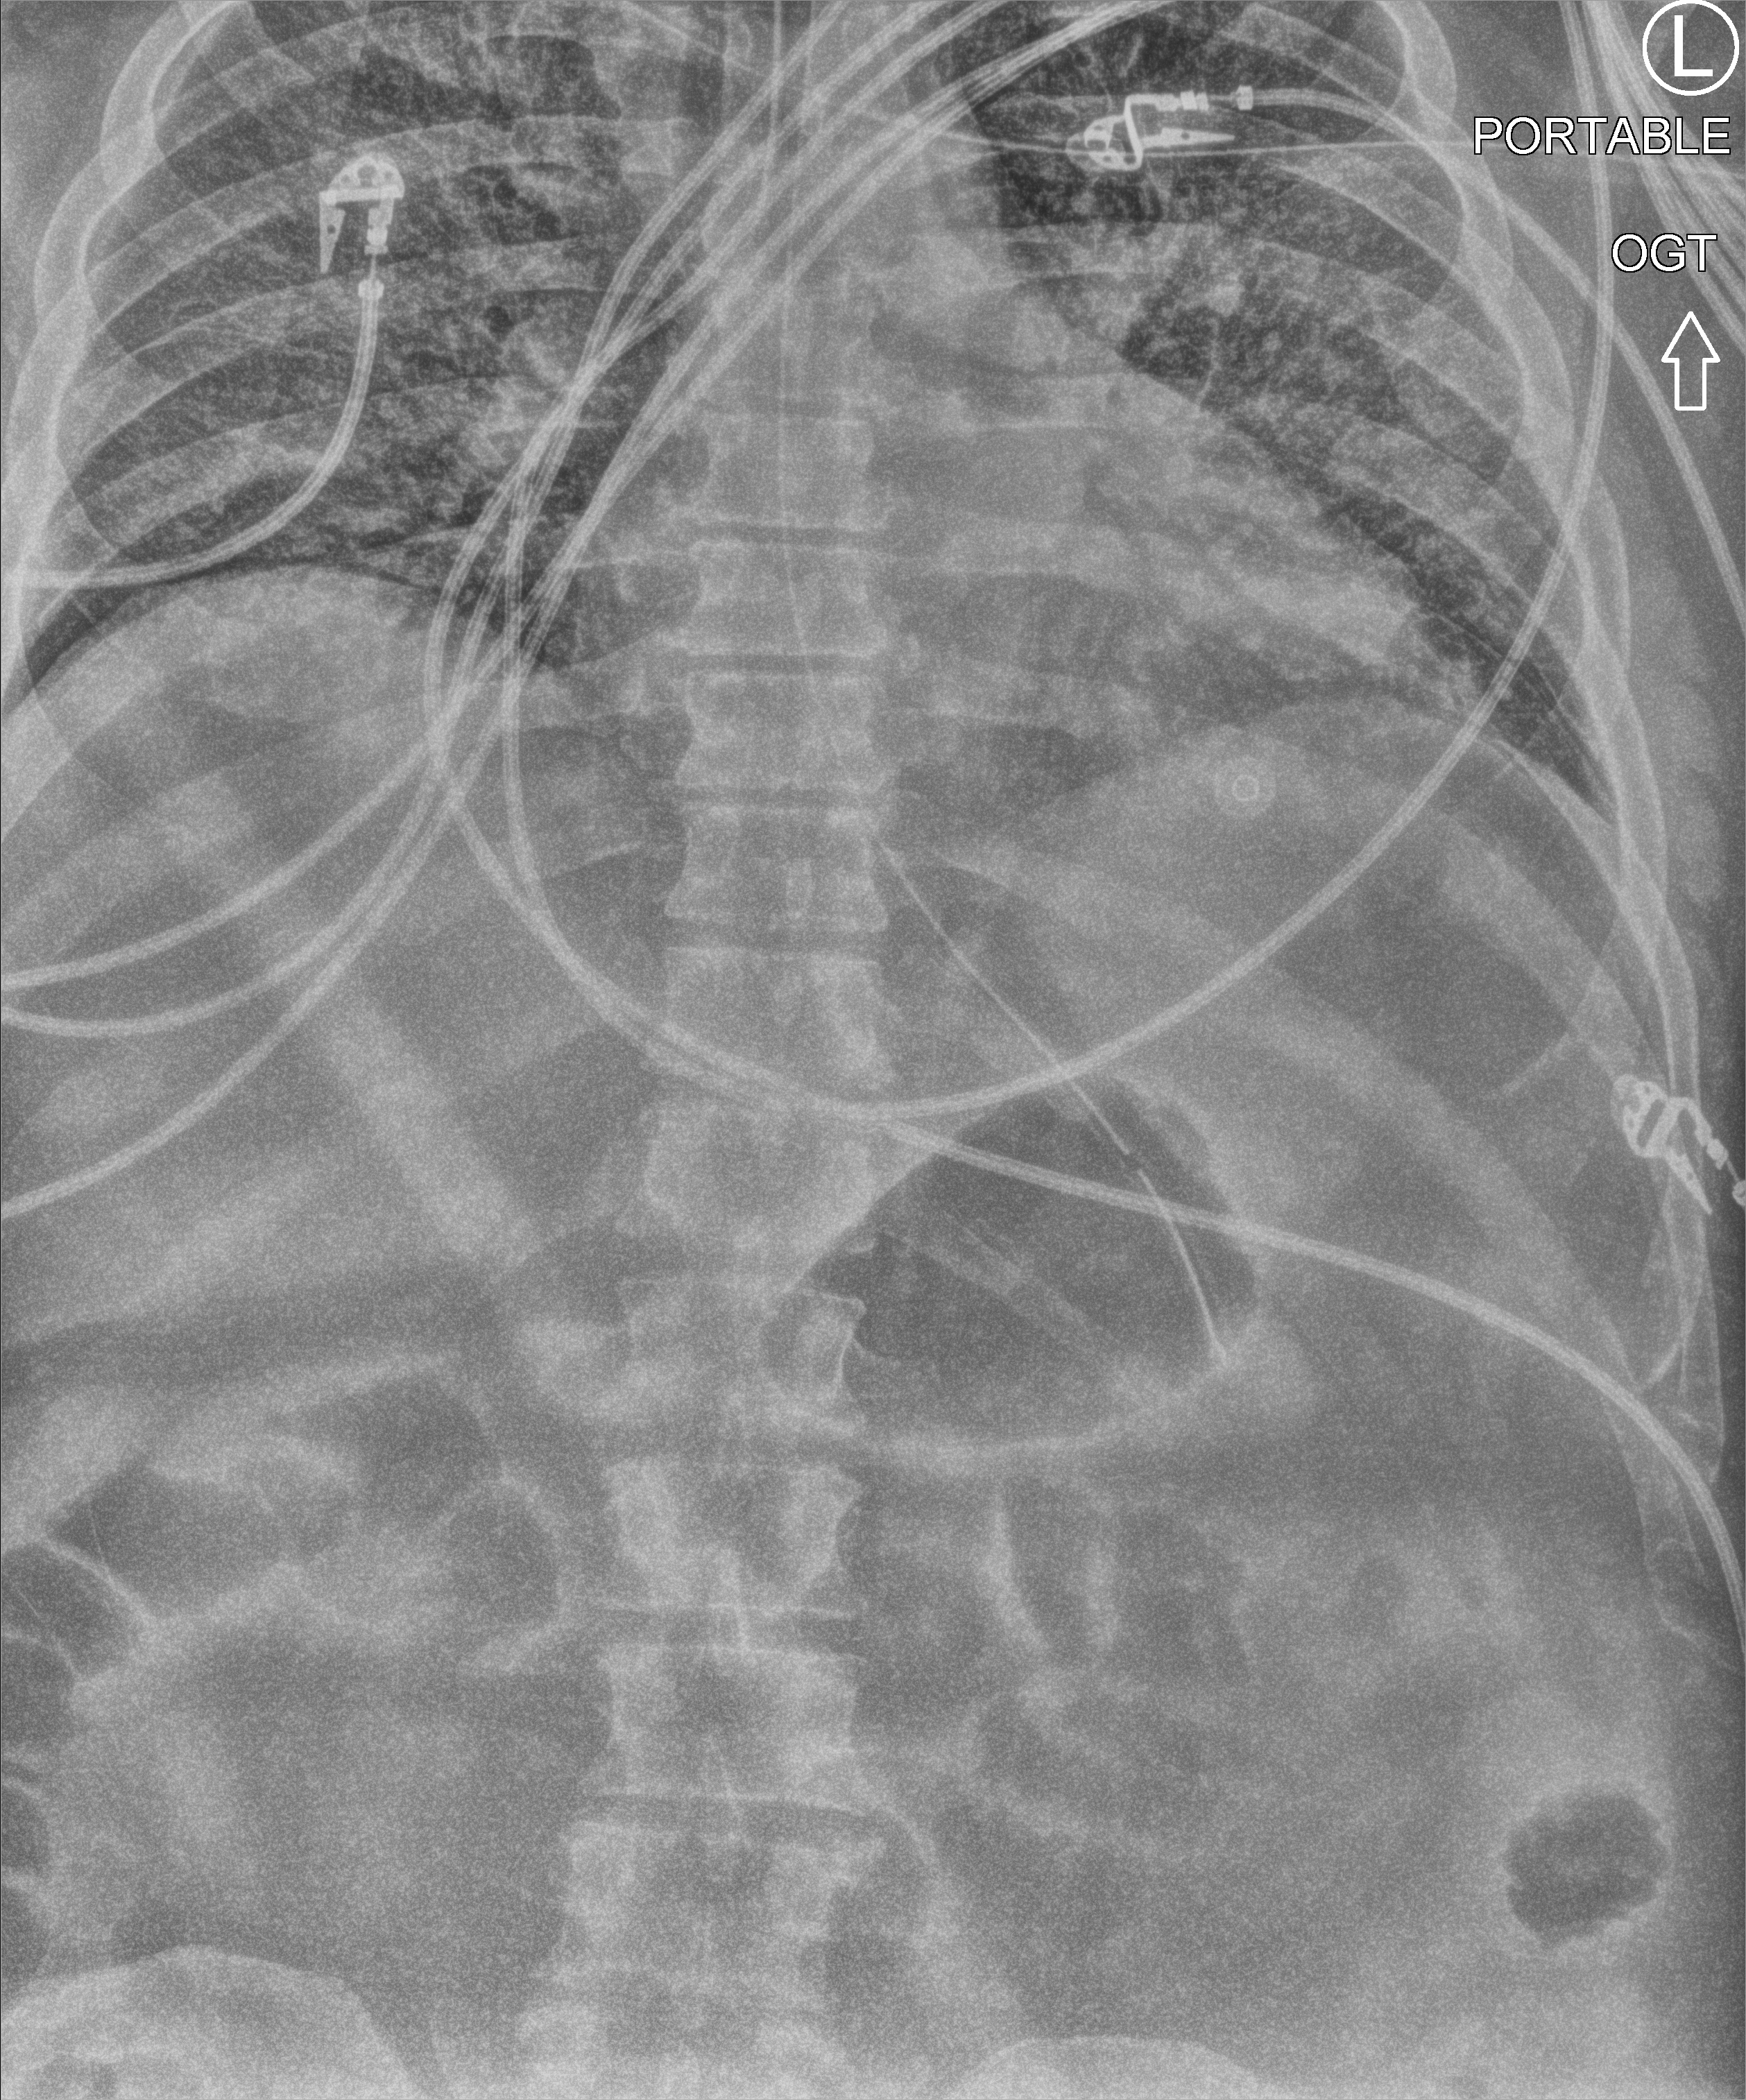
Bedside chest radiograph (computed radiography), anteroposterior (AP) projection. Male patient hospitalised with COVID-19, age 18–59 years.
Hospital-stay facts (about this admission, not read from this image; timing relative to this image not recorded): COPD (admission record): no; mechanically ventilated during this hospital stay: yes; length of hospital stay: 80 days.